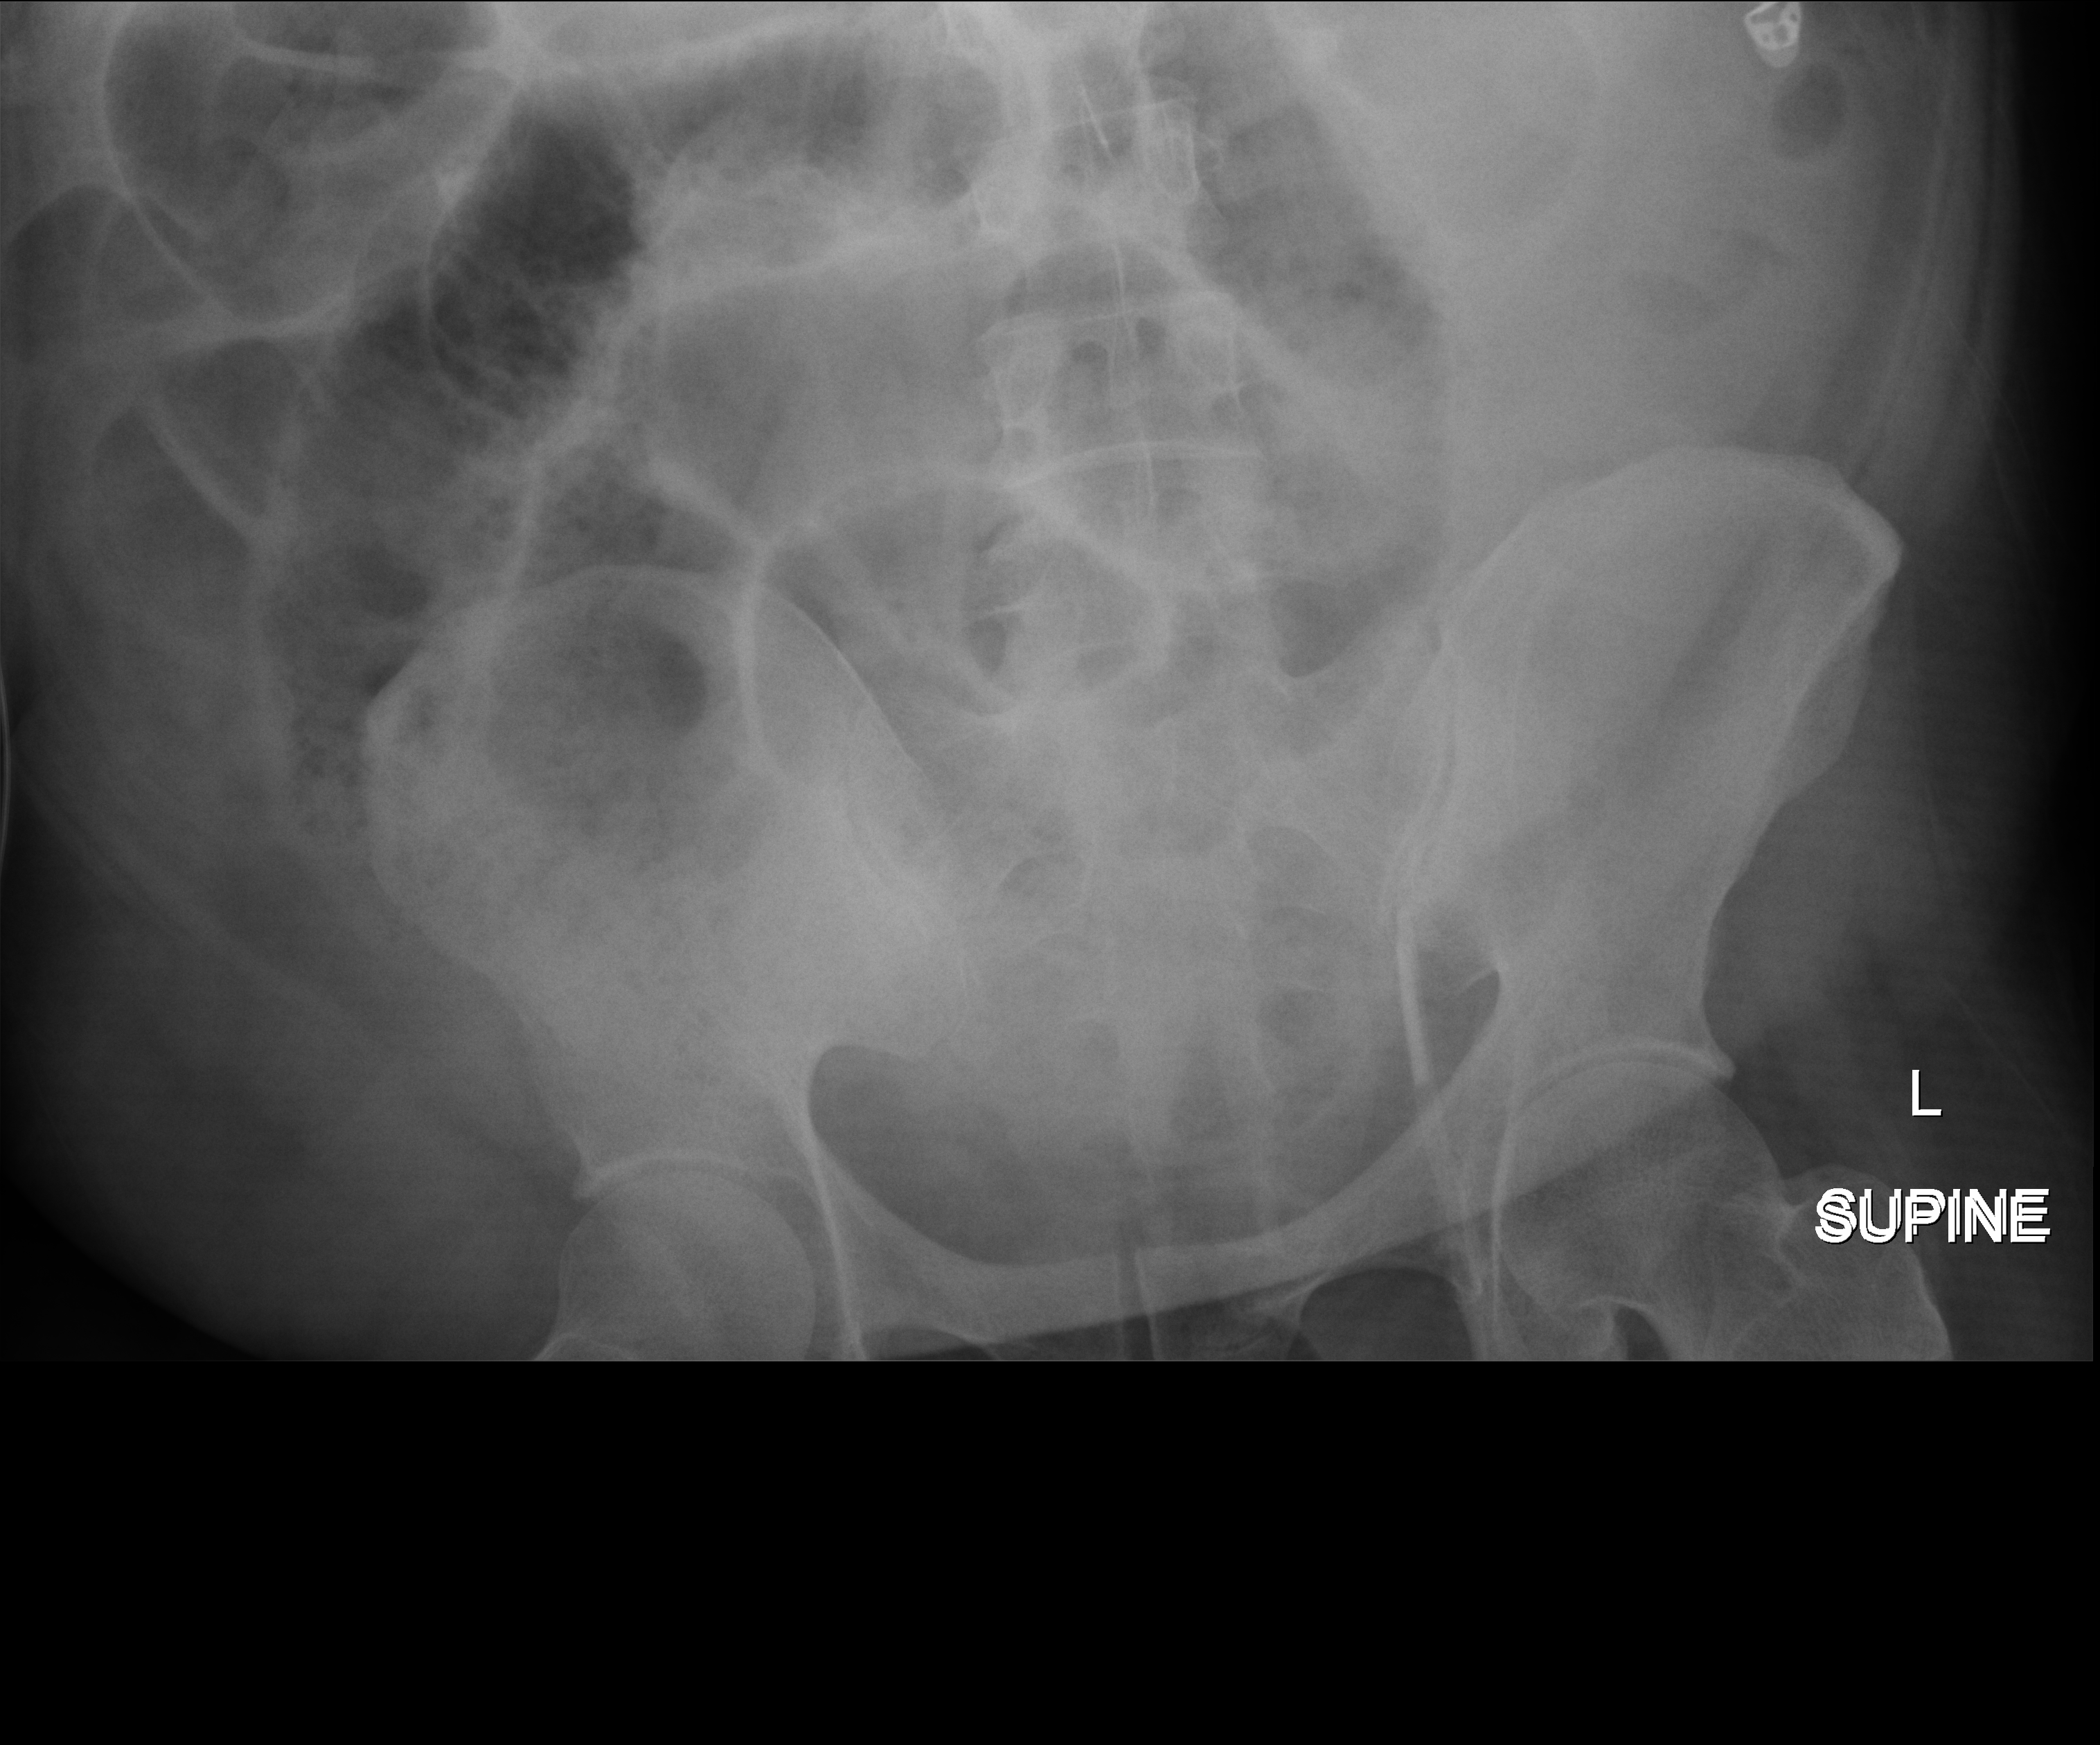
Abdomen X-ray (portable). Adult patient hospitalised with COVID-19, age 18–59 years.
Hospital-stay facts (about this admission, not read from this image; timing relative to this image not recorded): admitted to intensive care during this hospital stay: yes.